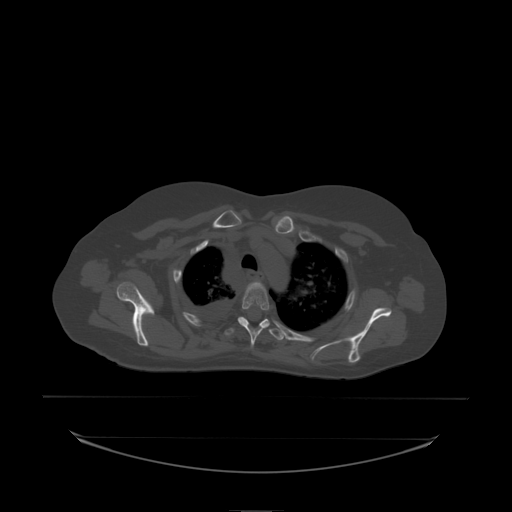
CT including the spine, one axial slice. Slice 172 of 242 in the series (ordered by position). Bone window (W 1800 / L 400 HU). 2.5 mm slice thickness. 512 × 512 image matrix. Patient: female, 53 years. From the clinical record (not read from this slice): primary cancer: lung; vertebrae with lytic lesions (as recorded): T7, L1.
Outlined on this slice (semi-automatic segmentation, software-assisted and operator-edited):
- T2 vertebra: bounding box <260,283,262,285> (left, top, right, bottom; pixels)
- T3 vertebra: <238,283,270,338>
- T4 vertebra: <229,317,282,337>